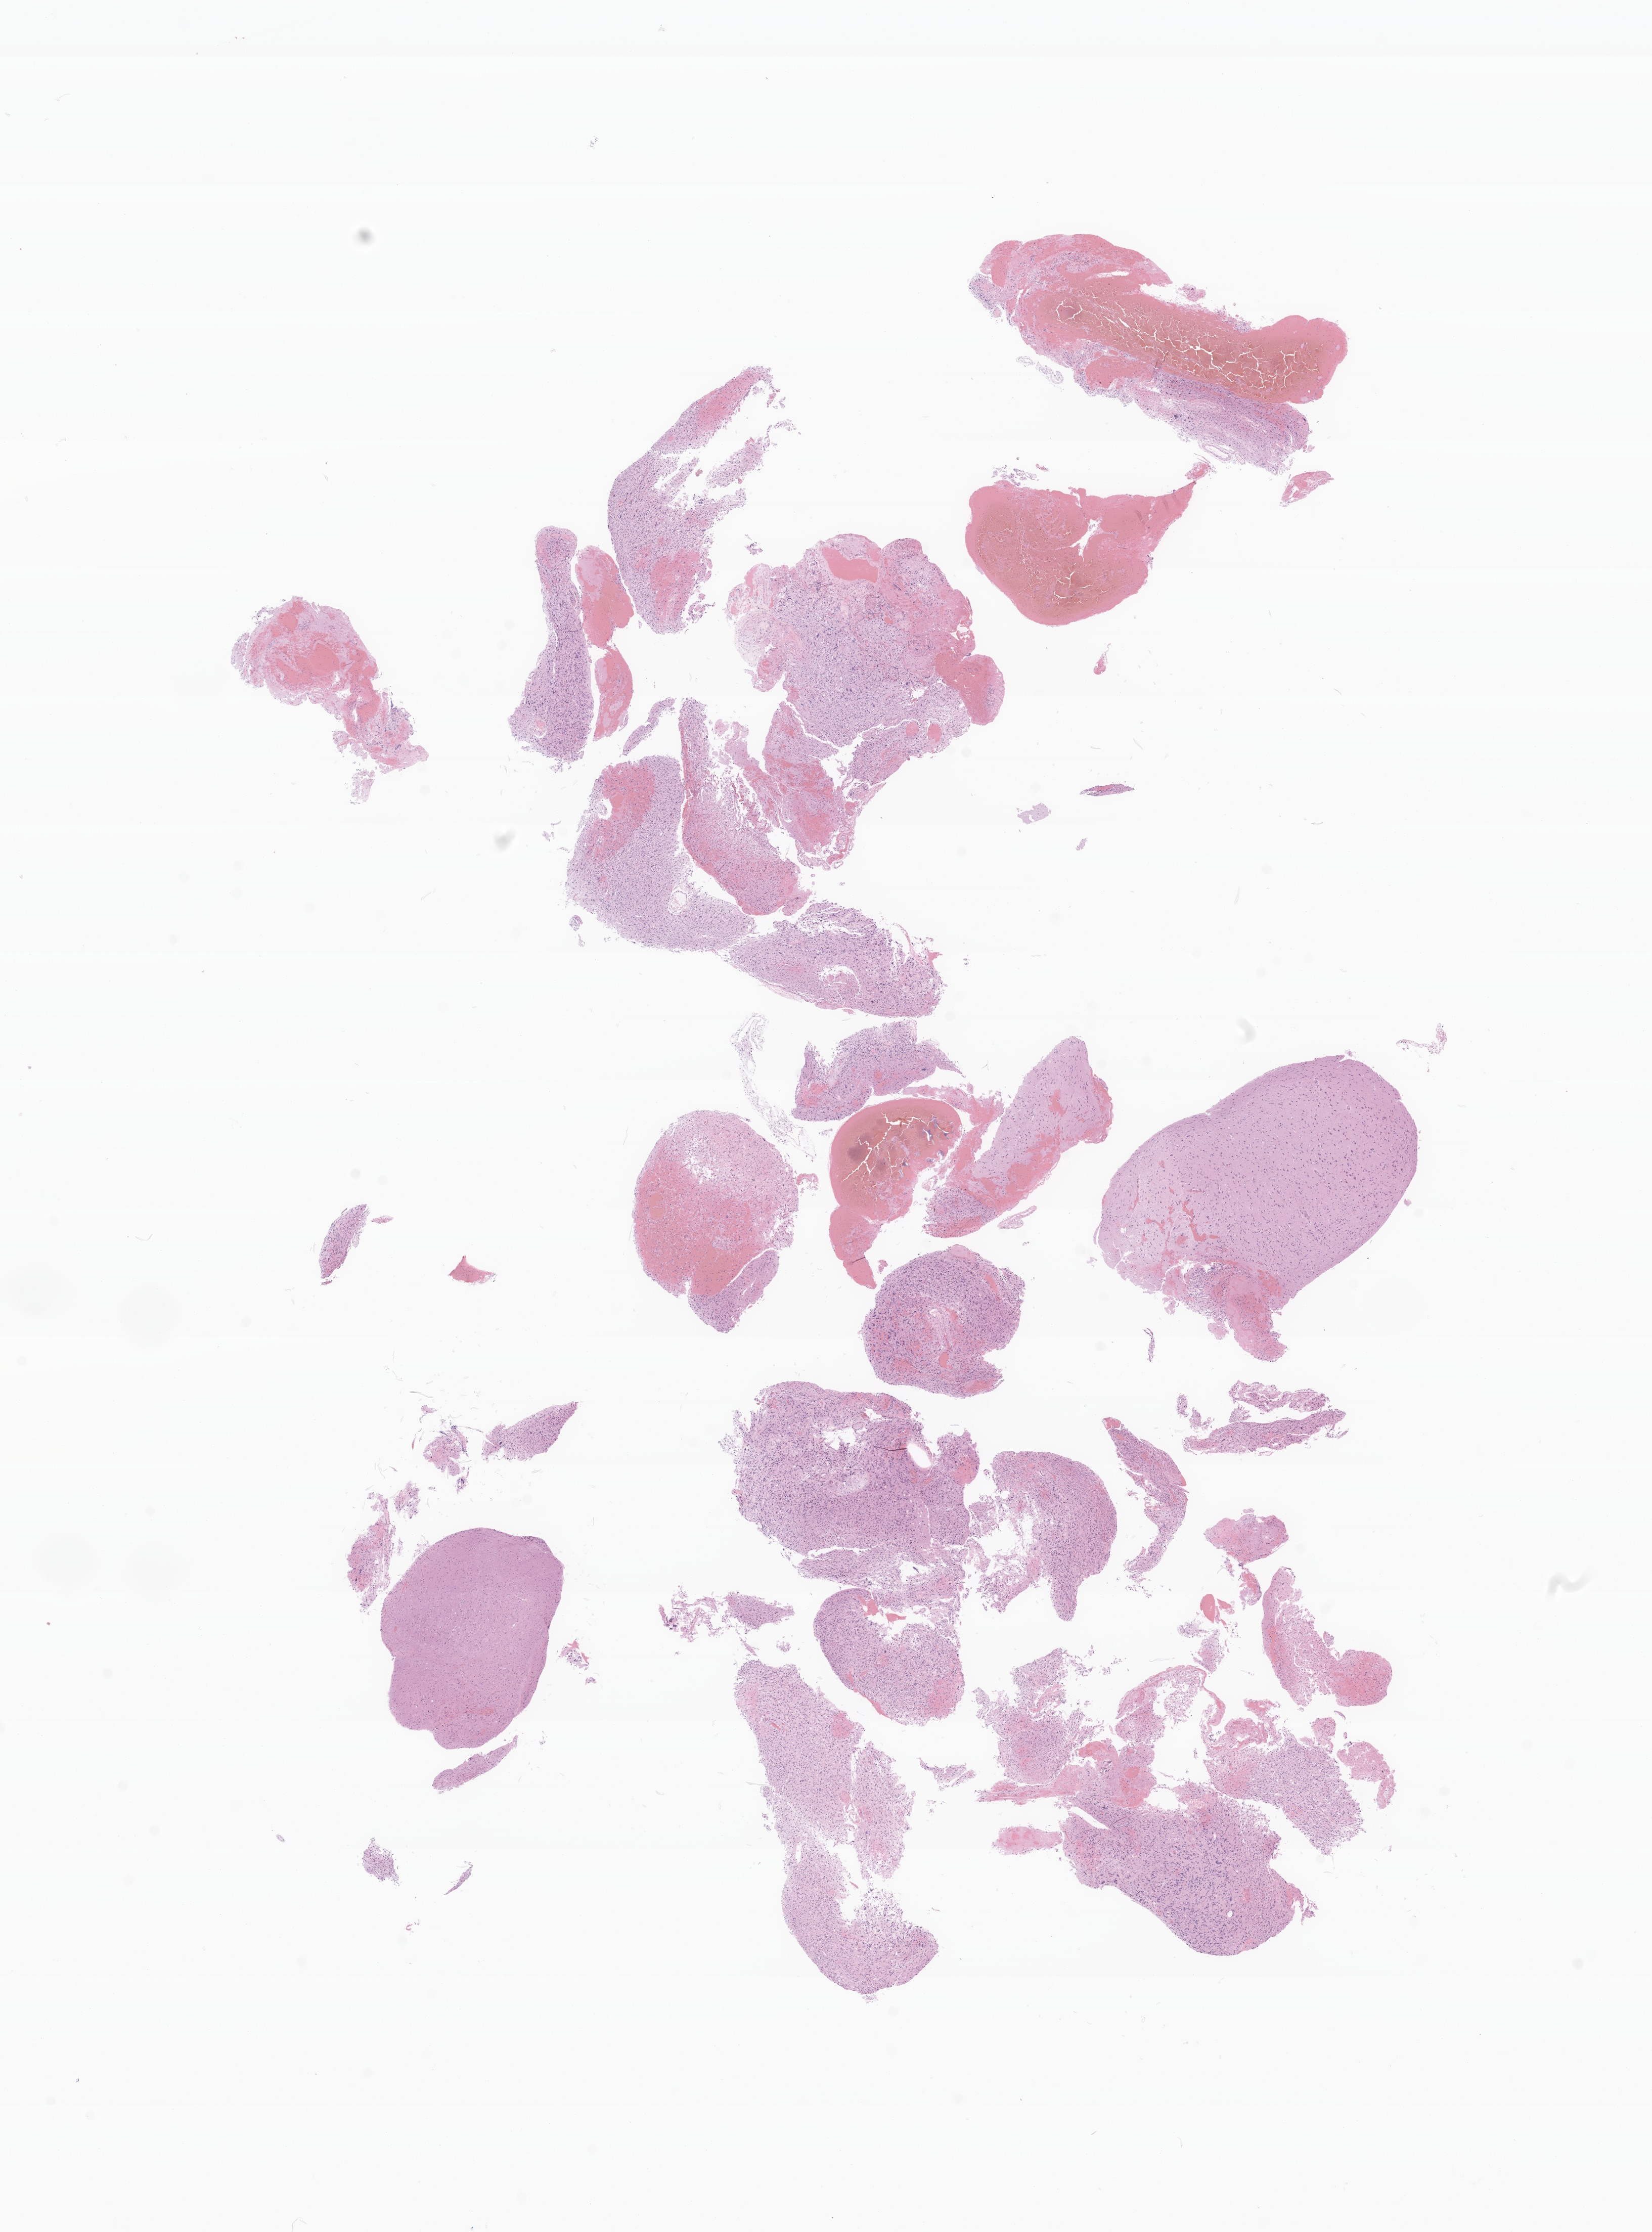
Whole-slide image, hematoxylin and eosin (H&E) stain of tumor tissue from the brain — a low-resolution overview of the entire scanned area, about 13.7 x 18.6 mm; formalin-fixed paraffin-embedded section. Female patient, age 129 months (10 years 9 months).
Diagnosis (ICD-O-3 morphology term): Glioma, malignant.